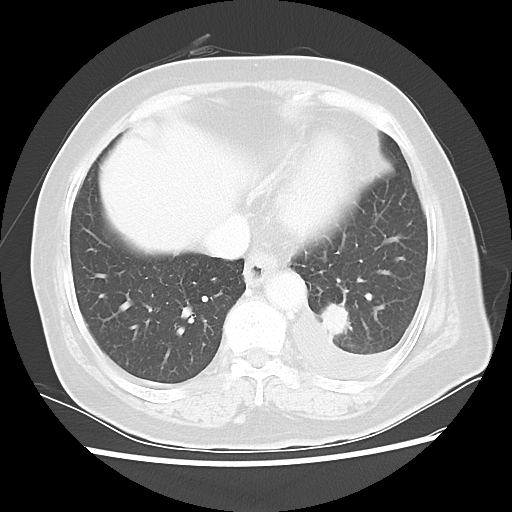
Chest CT, one axial slice. Slice 9 of 40 in the series (ordered by position). Lung window (W 1500 / L -600 HU). 5 mm slice thickness. 512 × 512 image matrix, field of view 343 × 343 mm. Female patient, age 68 years. Case-level facts recorded for this patient, not image findings: clinical TNM (as recorded): T1c N0 M1.
Outlined on this slice (bounding box drawn by a radiologist):
- lung tumour (recorded histology: adenocarcinoma): bounding box (x1, y1, x2, y2) in pixels: (317, 300, 354, 341)